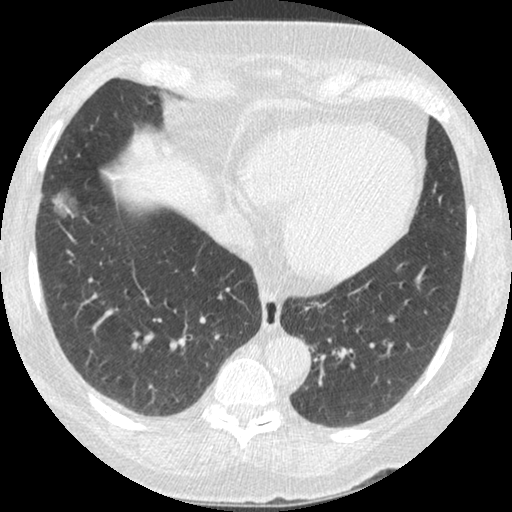
Low-dose screening chest CT, one axial slice. Slice 90 of 245 in the series (ordered by position). Reconstruction kernel STANDARD. 120 kVp. Lung window (W 1500 / L -600 HU). 1.25 mm slice thickness. 512 × 512 image matrix, field of view 310 × 310 mm.
Outlined on this slice (outlined manually by an expert reader):
- lesion 1 (tumor, lower lobe of right lung): box from (x=51, y=193) to (x=76, y=218) px